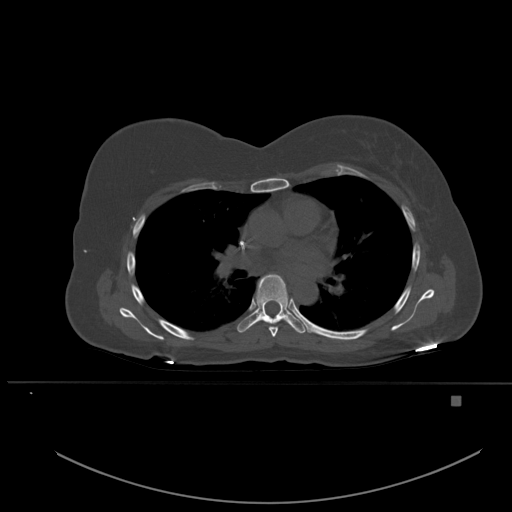
CT including the spine, one axial slice. Slice 355 of 651 in the series (ordered by position). Bone window (W 1800 / L 400 HU). 1.5 mm slice thickness. 512 × 512 image matrix, field of view 443 × 443 mm. Female patient, age 49 years. From the clinical record (not read from this slice): primary cancer: breast; vertebrae with lytic lesions (as recorded): L3, T12, L4.
Annotated regions visible in this slice (semi-automatic segmentation, software-assisted and operator-edited):
- T5 vertebra: bounding box <269,326,278,337> (left, top, right, bottom; pixels)
- T6 vertebra: <237,274,306,334>